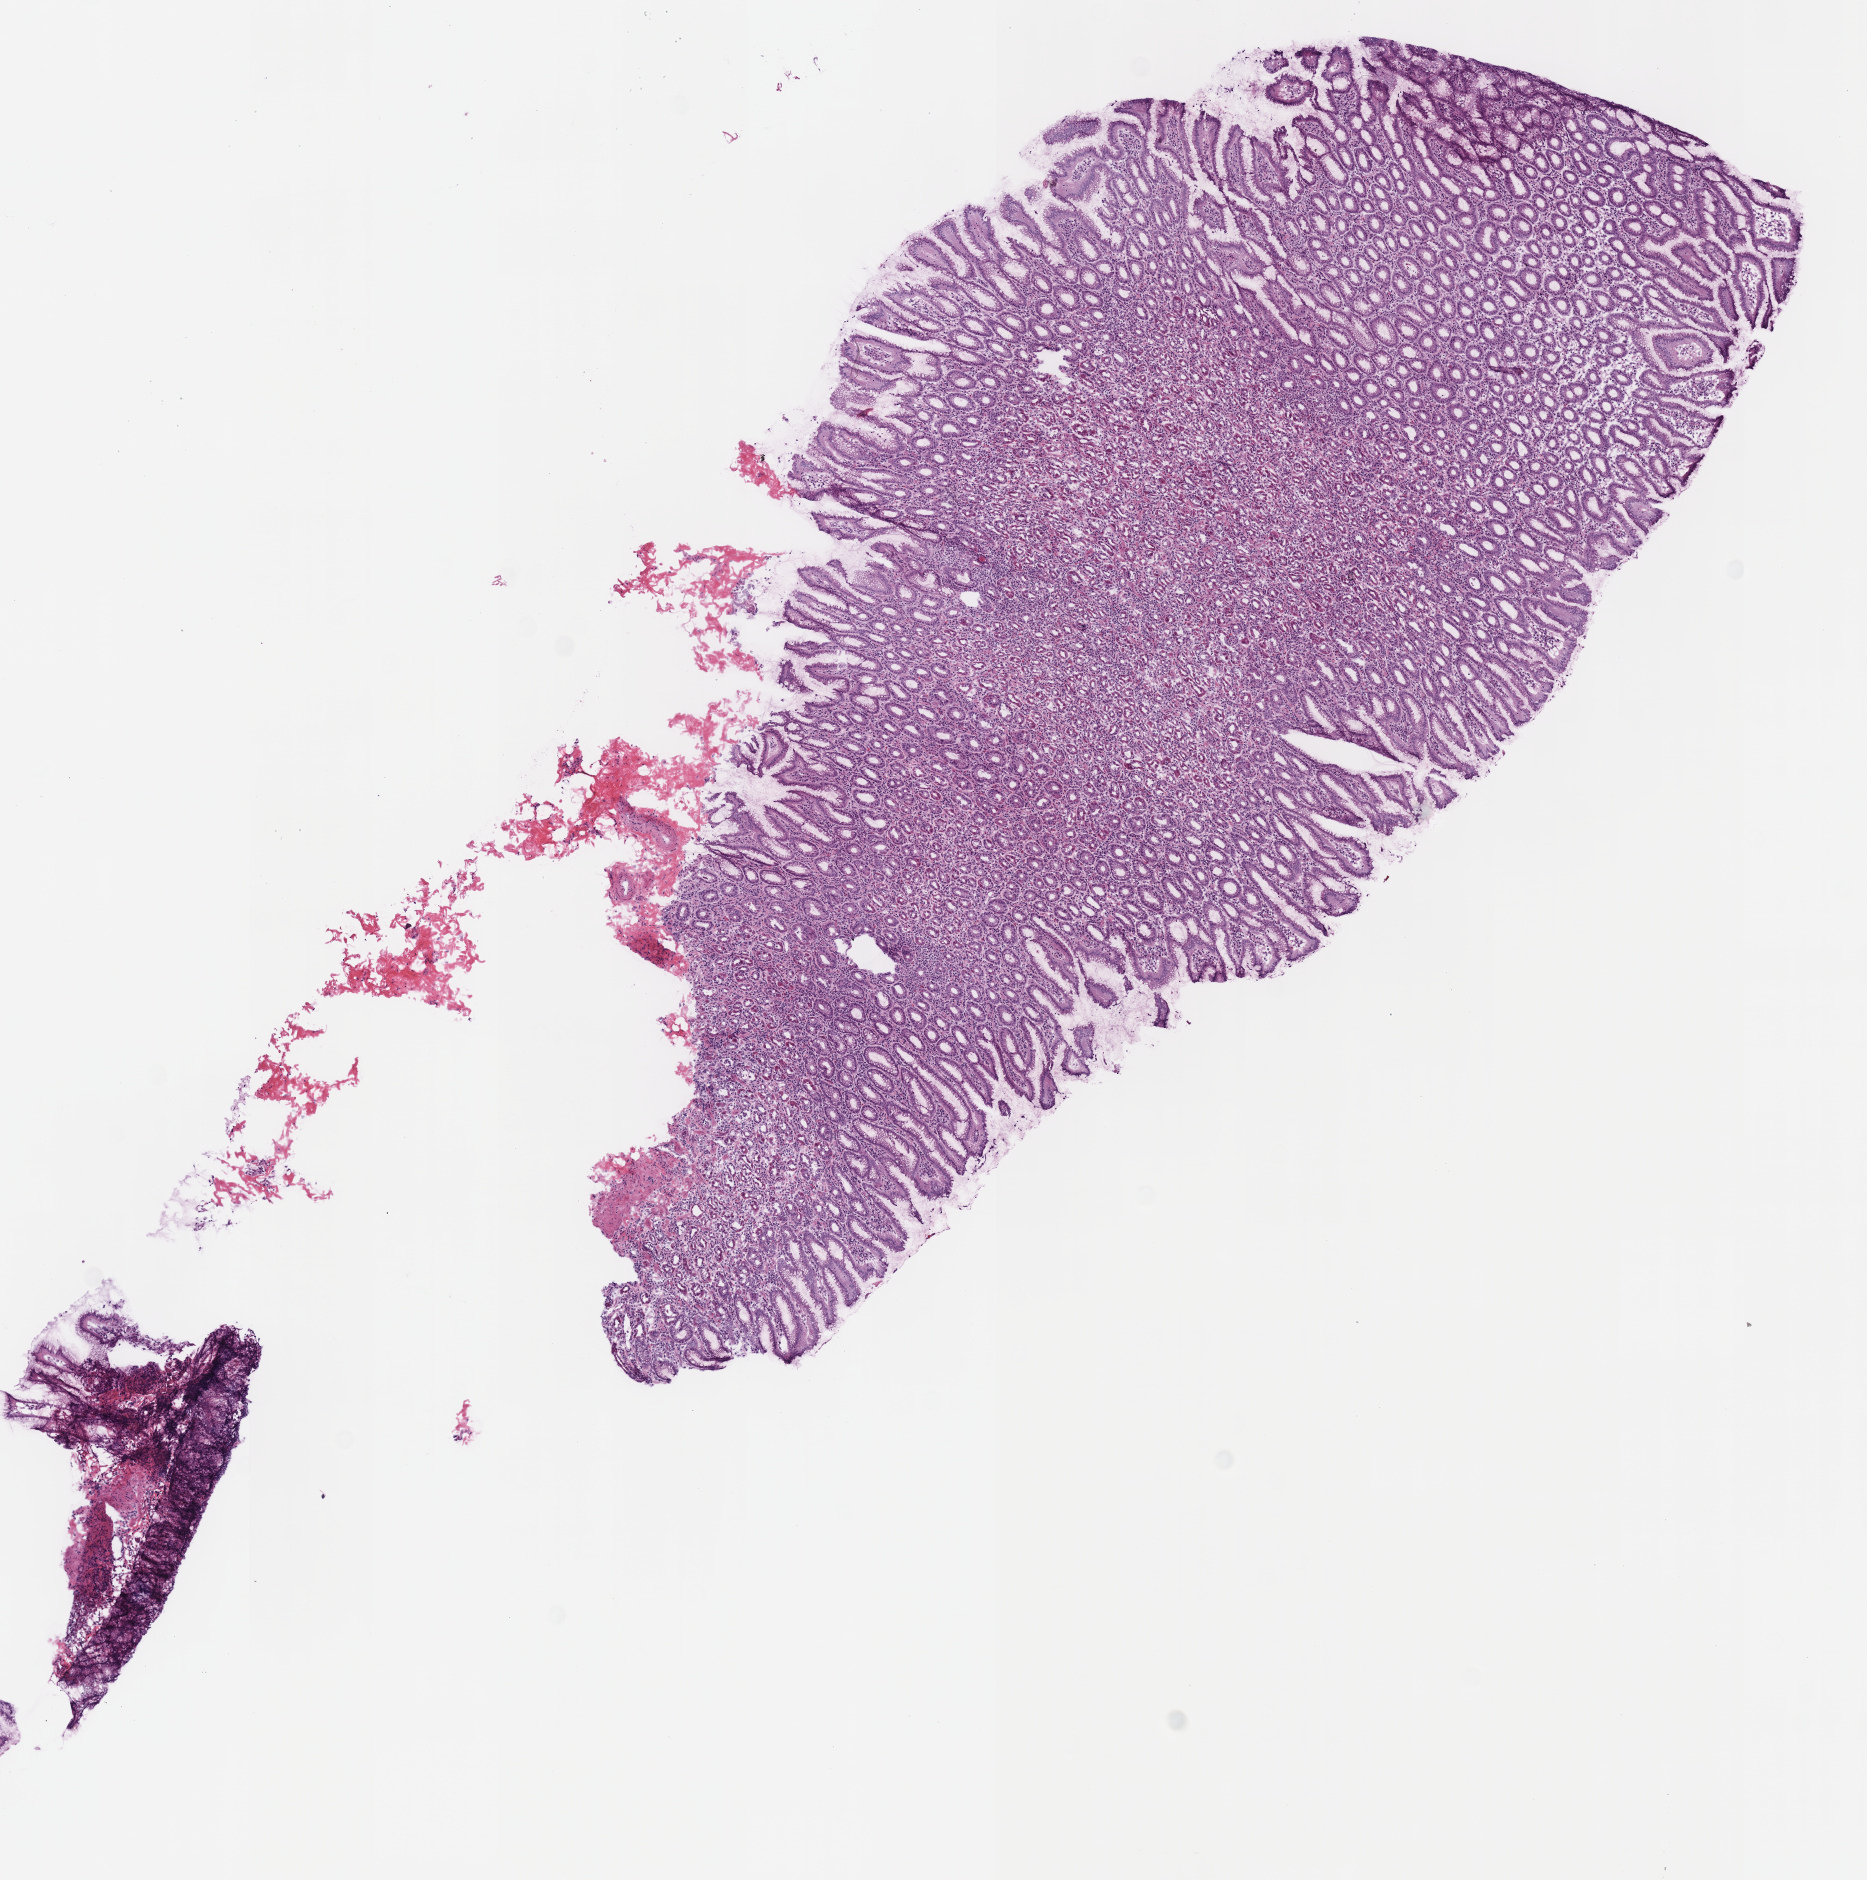
Digitized Hematoxylin and eosin (H&E) stained tissue section (whole slide) — a low-resolution overview of the entire scanned area, about 7.3 x 7.4 mm; frozen section from the top of the tissue portion; stomach, solid tissue normal (non-tumour tissue) sample. Patient: female, age at initial diagnosis 58 years.
This section: solid tissue normal (non-tumour) sample from the same patient. Patient diagnosis: Carcinoma, diffuse type.